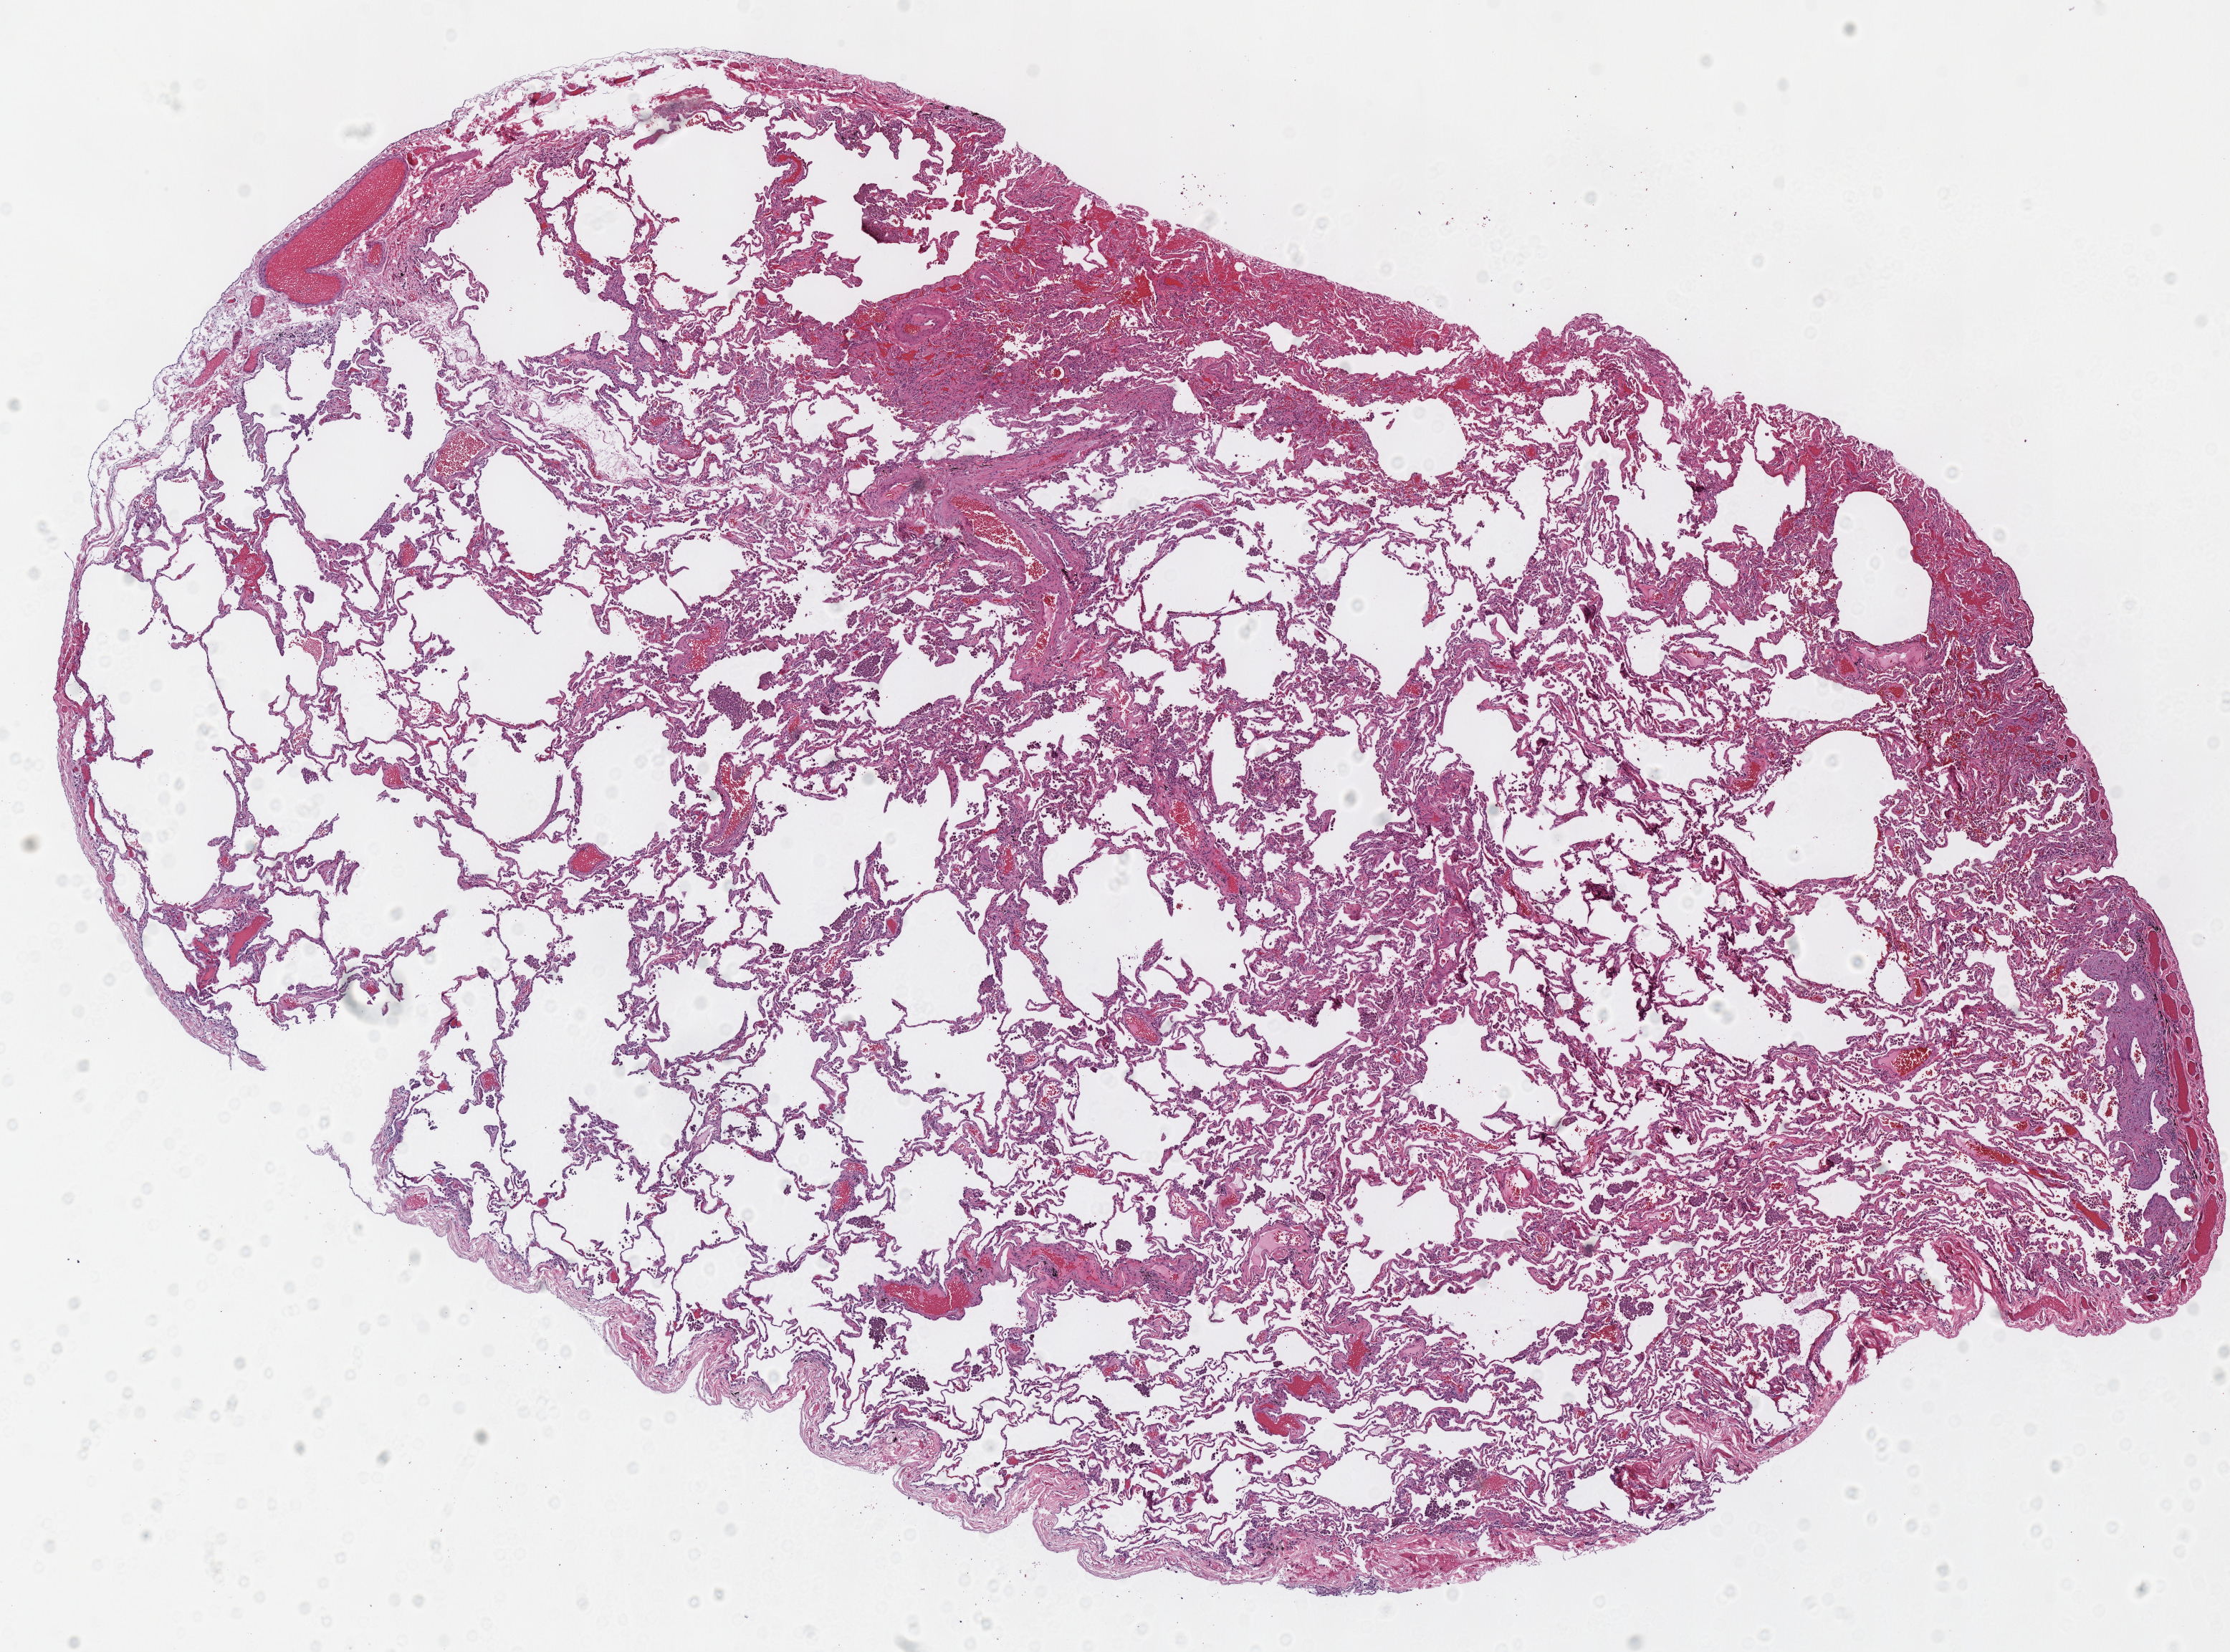
Digitized Hematoxylin and eosin (H&E) stained tissue section (whole slide) — low-resolution overview of the scanned area, about 12.2 x 9.1 mm; frozen section from the top of the tissue portion; solid tissue normal (non-tumour tissue) sample from the lung. Female patient; age at initial diagnosis 52 years.
This section: solid tissue normal (non-tumour) sample from the same patient. Patient diagnosis: Adenocarcinoma, NOS (upper lobe, lung).